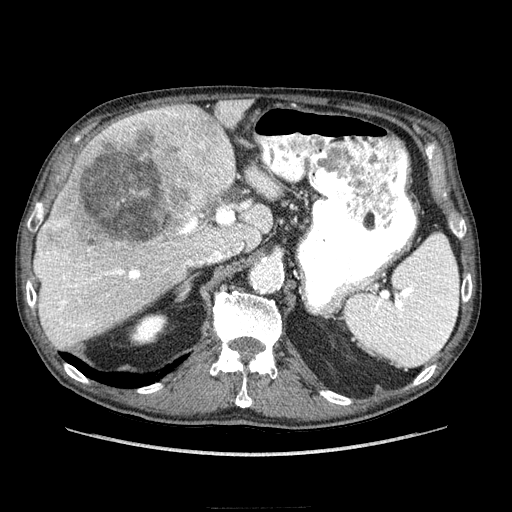
Contrast-enhanced abdominal CT (liver protocol), one axial slice; position 153 of 218 along the scan axis; reconstruction kernel STANDARD; 100 kVp; soft-tissue window (W 400 / L 40 HU); 512 × 512 image matrix, field of view 380 × 380 mm. From the clinical record (not read from this slice): diagnosis: hepatocellular carcinoma (patient treated with transarterial chemoembolisation; whether this scan precedes or follows treatment is not stated here); TNM stage (as recorded): Stage-IIIA; Child-Pugh class: A.
Annotated regions visible in this slice (semi-automatically segmented with operator editing):
- liver parenchyma outside the tumour (the mass and vessels are separate outlines, so this box may not span the whole liver): bounding box (x1, y1, x2, y2) in pixels: (34, 100, 278, 348)
- mass: (46, 105, 236, 265)
- liver vessels: (37, 119, 274, 331)